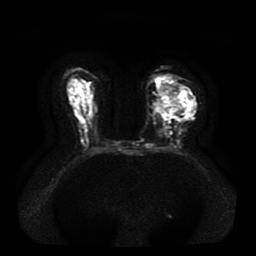
Breast MRI, one axial slice; position 22 of 41 along the scan axis; diffusion-weighted series; image 2 of 4 stored at this slice position (different b-values; order by instance number); 1.5 T; 256 × 256 image matrix. Female patient.
Annotated regions visible in this slice (manually delineated by an expert):
- tumour on diffusion-weighted imaging: box from (x=156, y=91) to (x=184, y=114) px